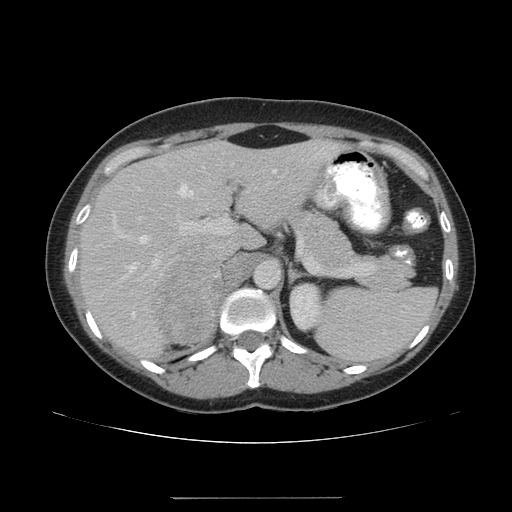
Contrast-enhanced abdominal CT, one axial slice. 120 kVp. Intravenous contrast given. Soft-tissue window (W 400 / L 40 HU). 3.75 mm slice thickness. 512 × 512 image matrix, field of view 380 × 380 mm. Female patient. From the clinical record (not read from this slice): diagnosis: adrenocortical carcinoma; tumour side: right adrenal.
Annotated regions visible in this slice (semi-automatically segmented with operator editing):
- mass: bounding box (x1, y1, x2, y2) in pixels: (153, 263, 220, 341)